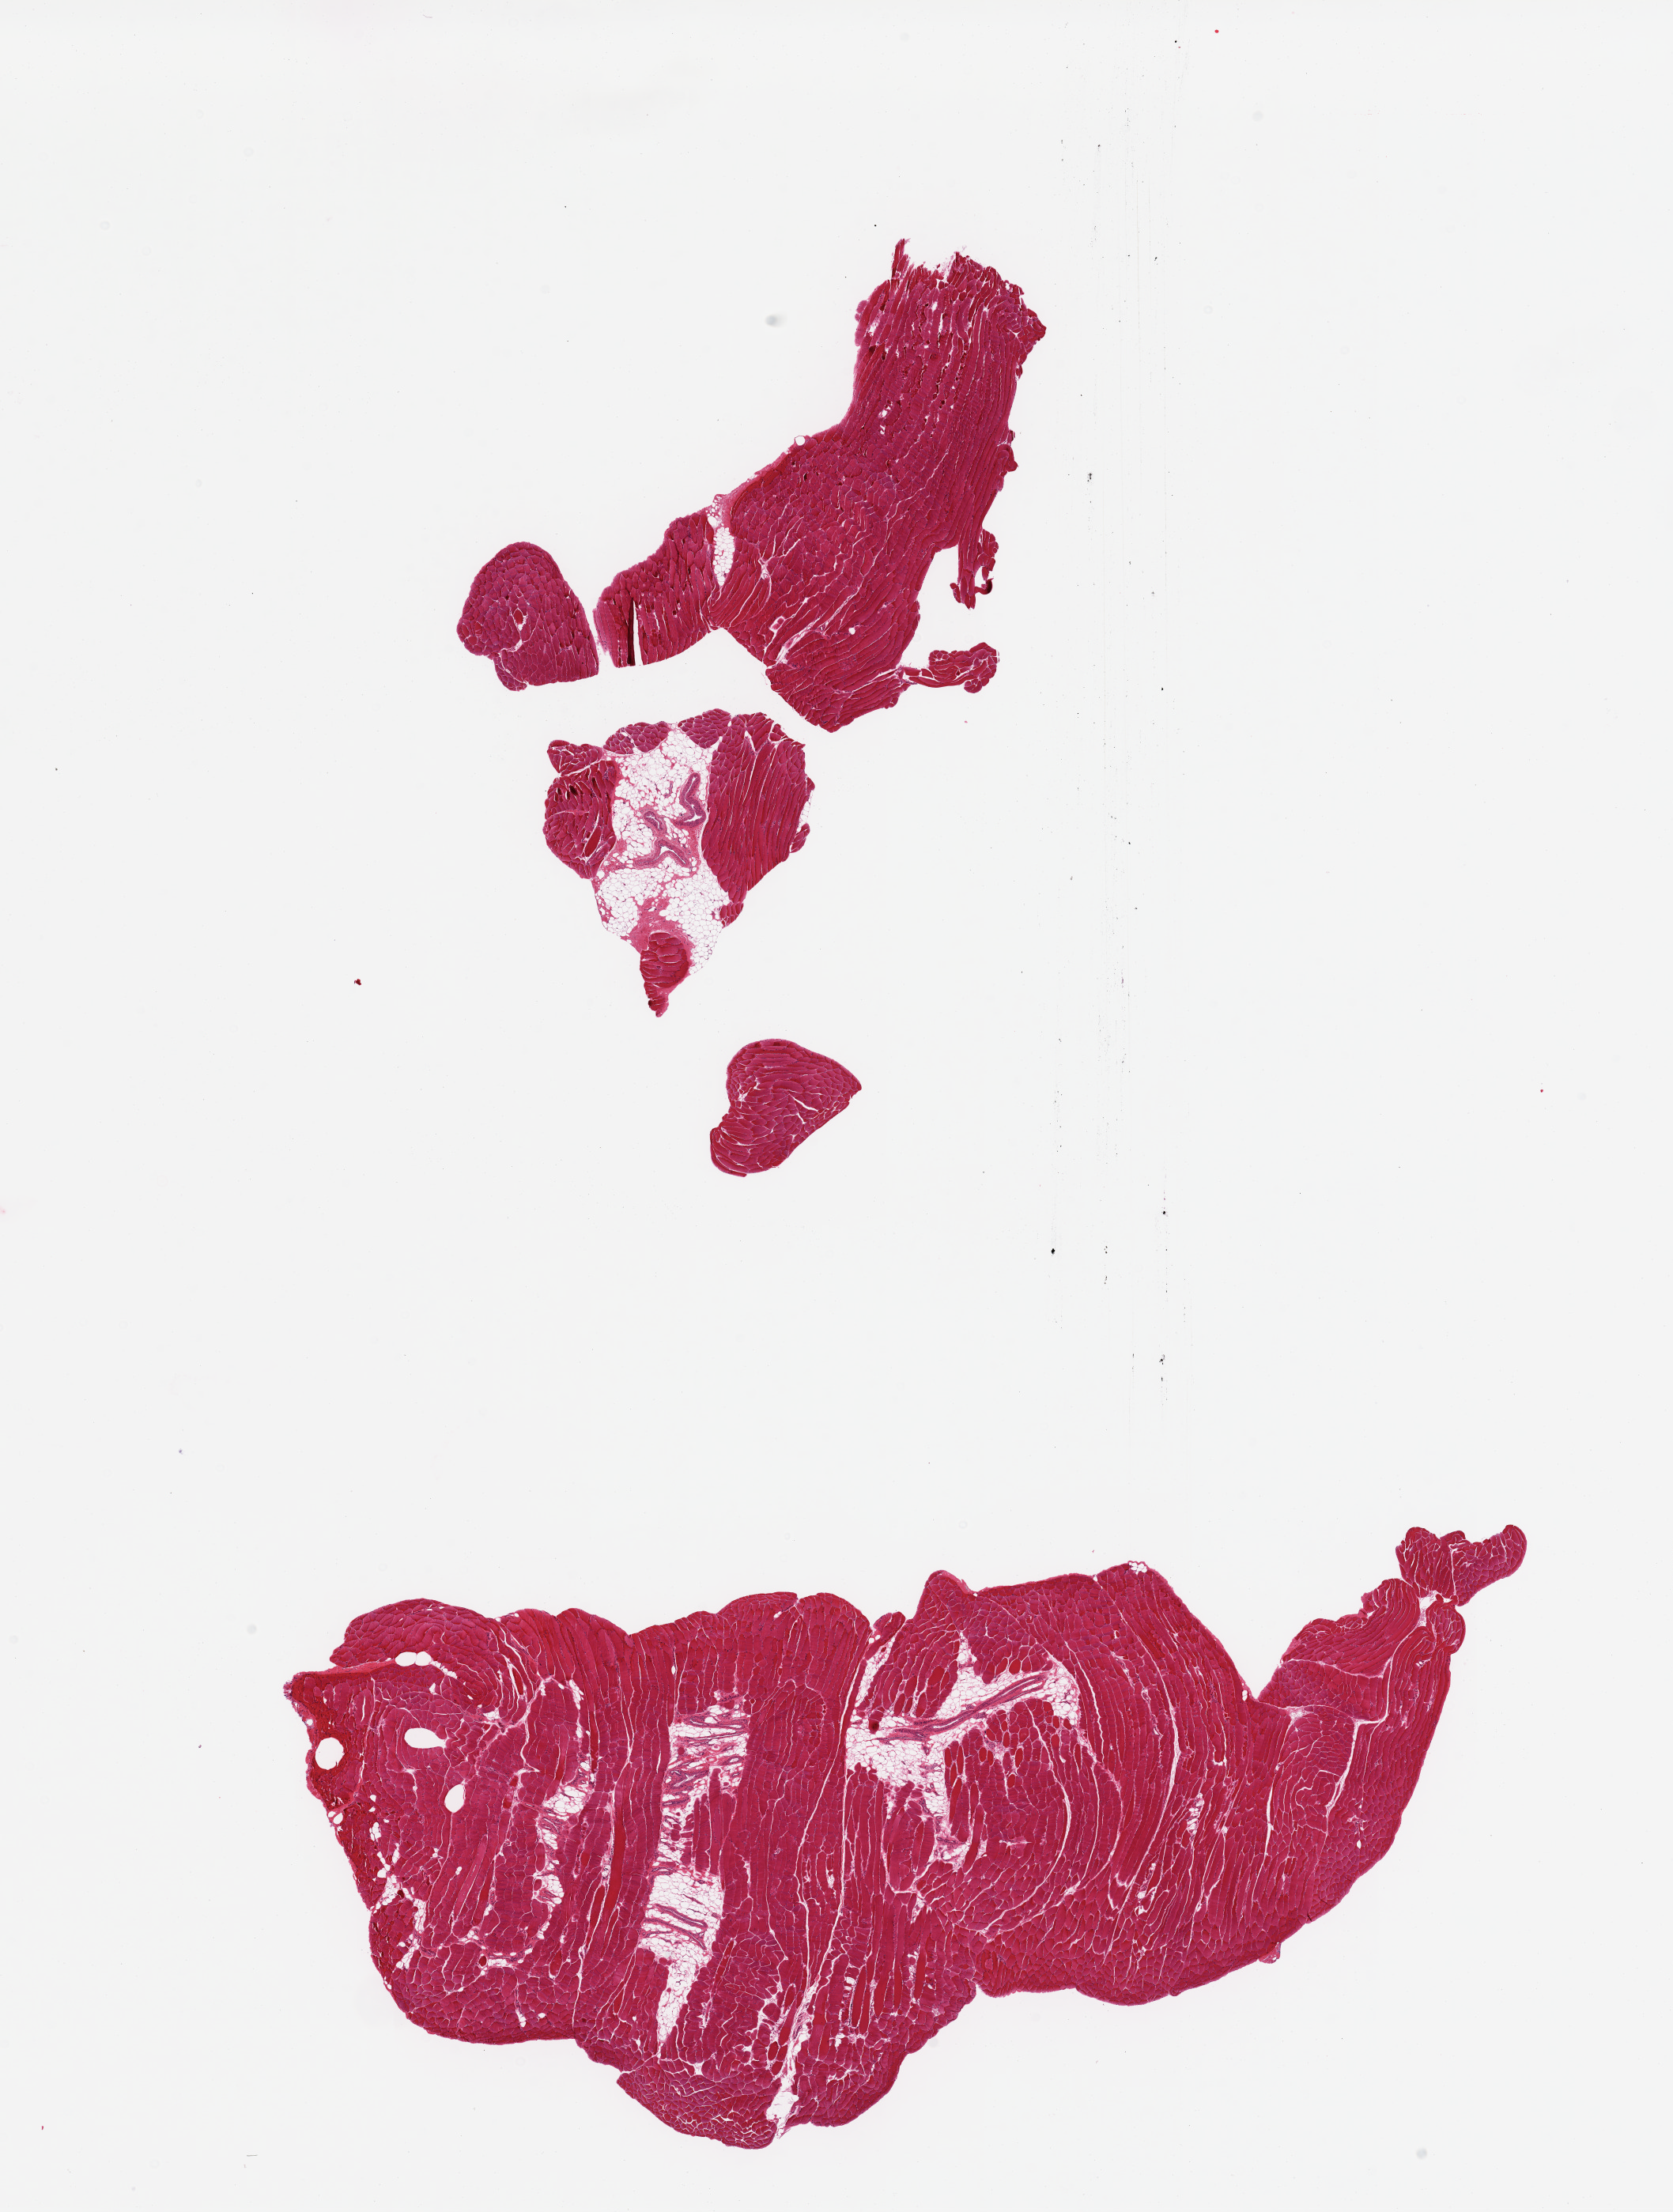
Whole-slide image, H&E stain, brightfield, shown as a low-resolution overview of the whole scanned area (about 16.7 x 22.1 mm), PAXgene-fixed, paraffin-embedded tissue, target tissue: skeletal muscle, donor tissue sample.
* pathologist's review note for this sample: 2 pieces, ~10% interstitial/vascular elements